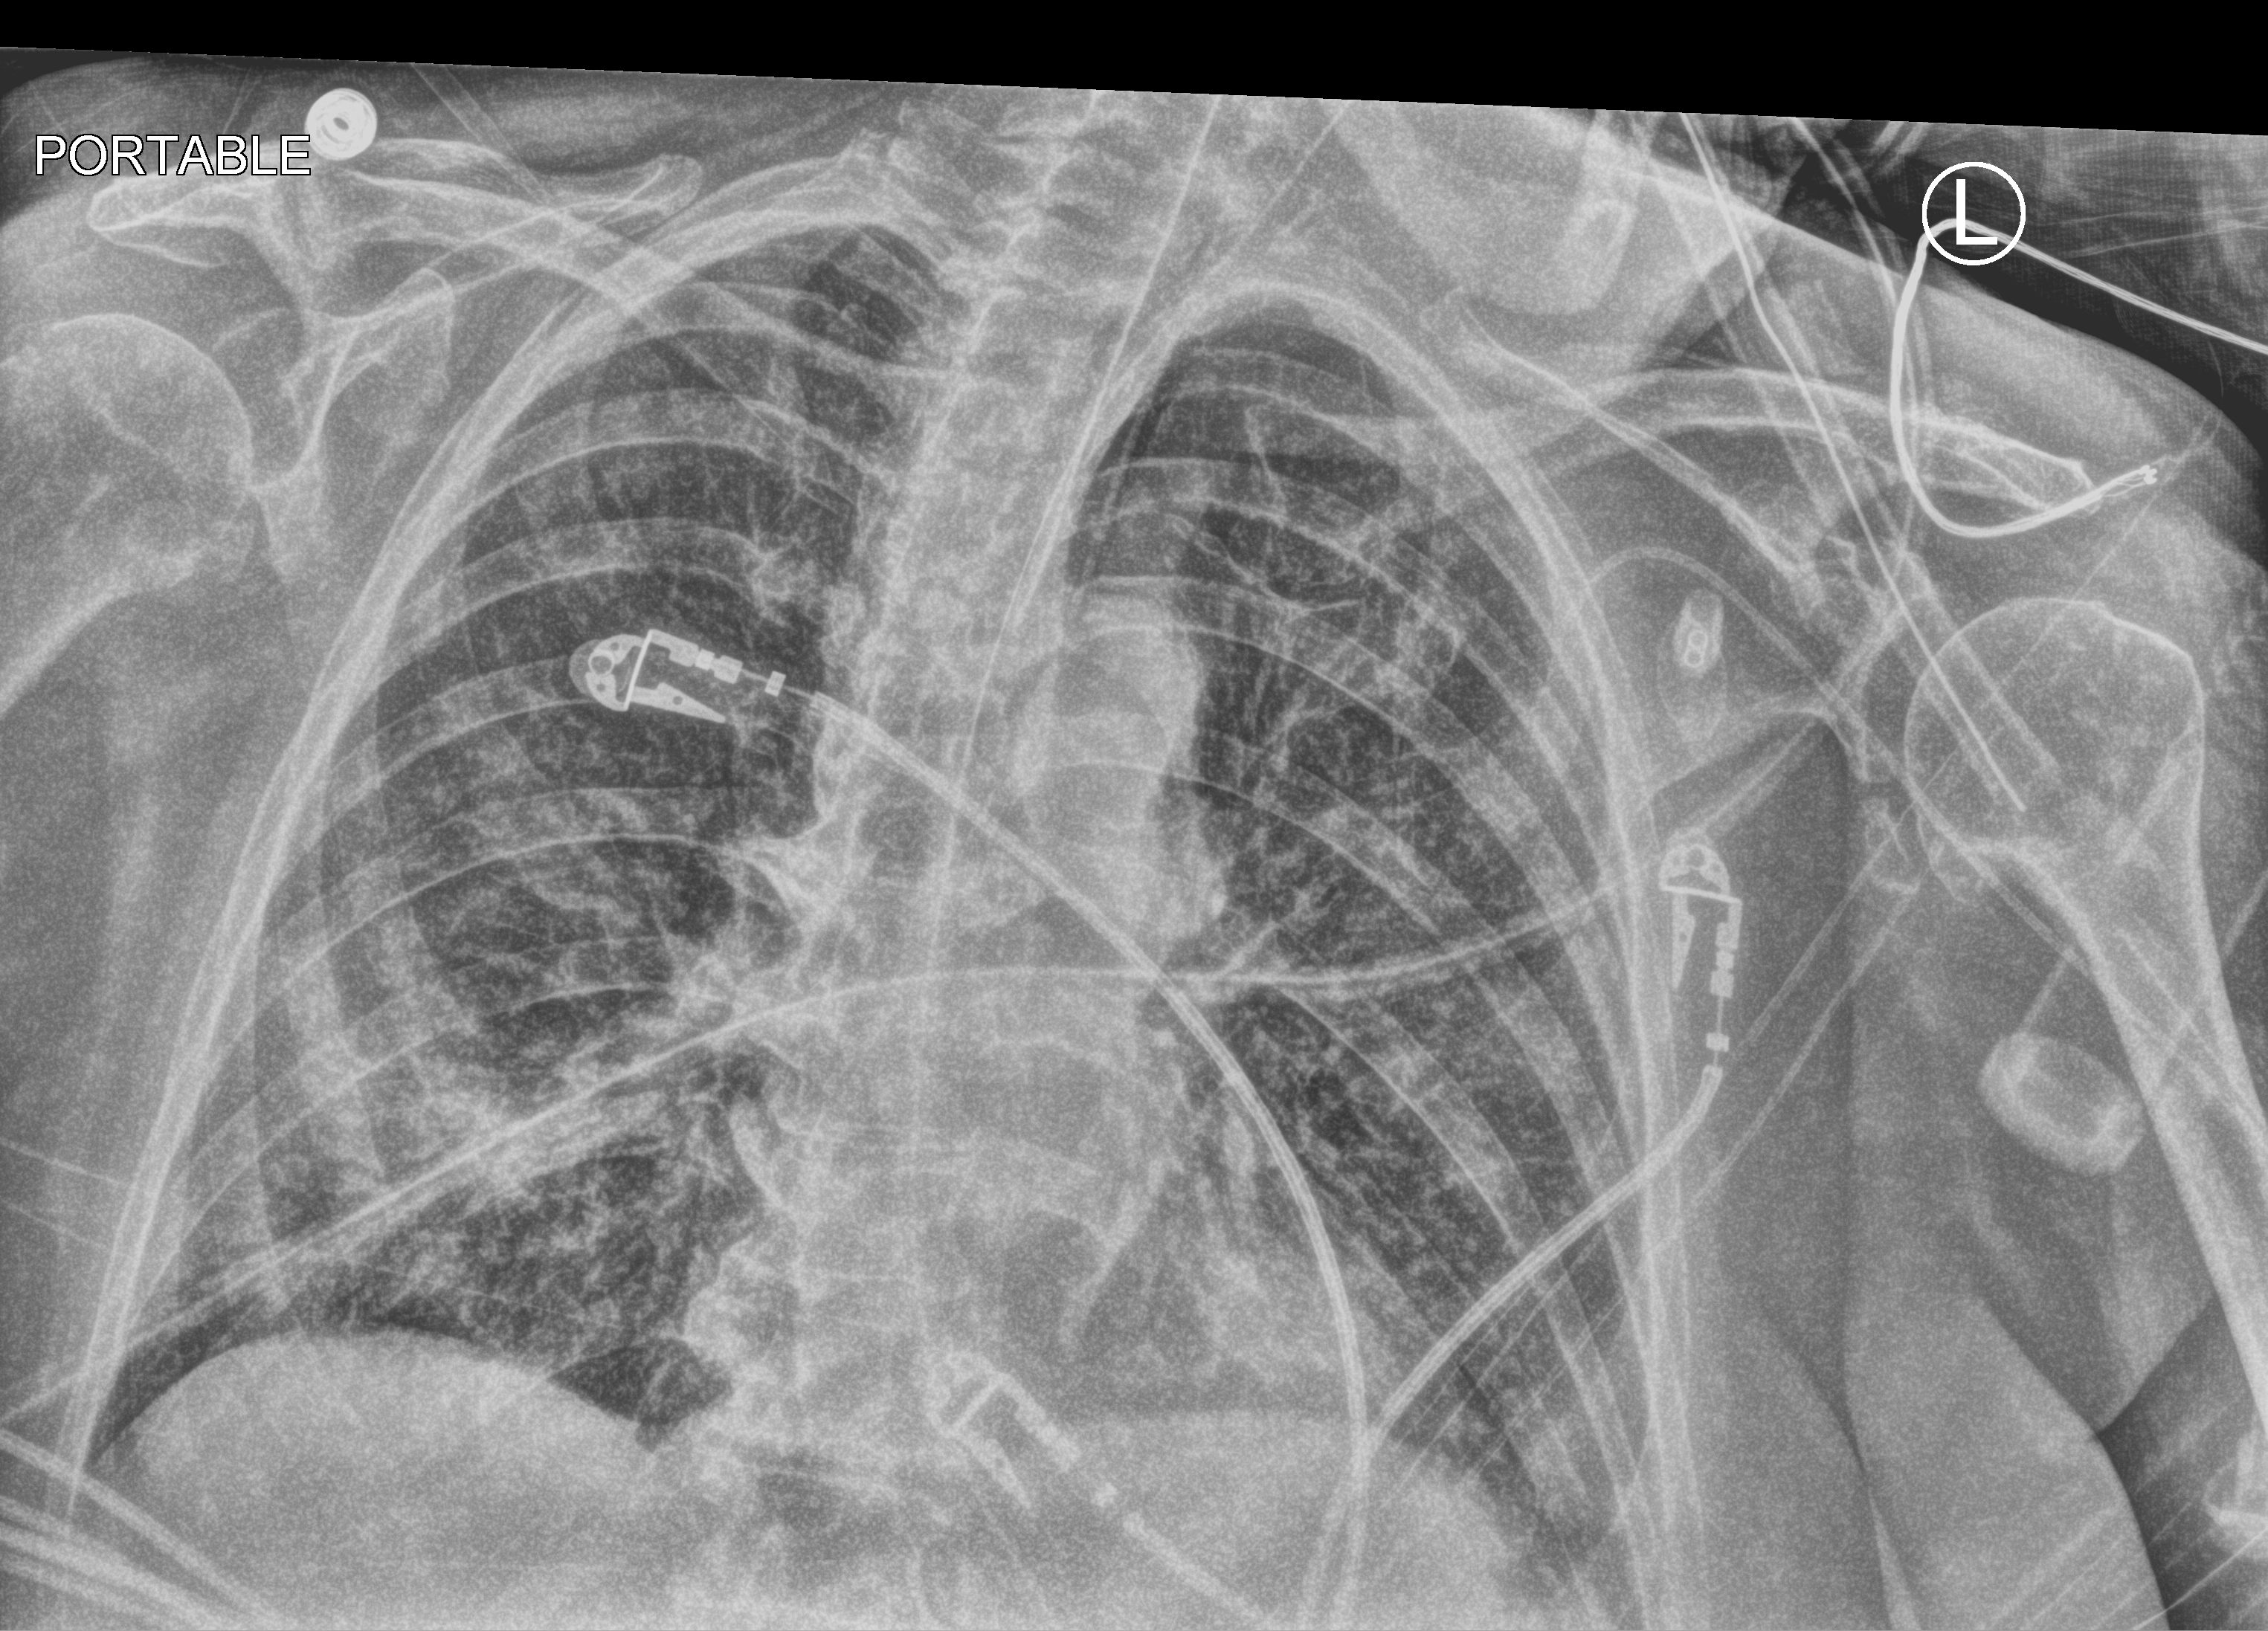
Bedside chest radiograph (computed radiography), anteroposterior (AP) projection. Patient hospitalised with COVID-19; female, aged 75–90 years.
Hospital-stay facts (about this admission, not read from this image; timing relative to this image not recorded): admitted to intensive care during this hospital stay: no; other chronic lung disease (admission record): no; chronic kidney disease (admission record): no.